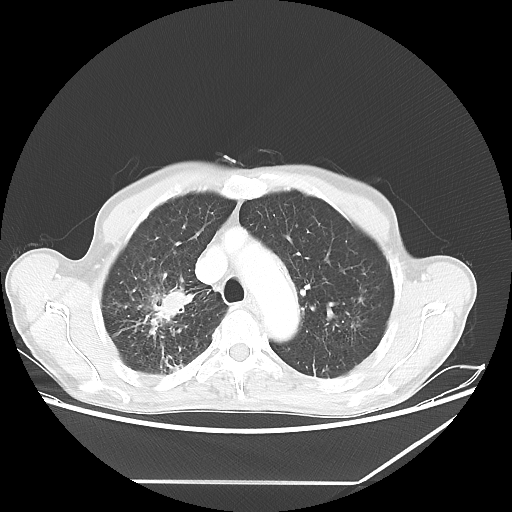
Chest CT, one axial slice. Position 48 of 65 along the scan axis. Reconstruction kernel LUNG. 80 kVp. Lung window (W 1500 / L -600 HU). 5 mm slice thickness. 512 × 512 image matrix, field of view 397 × 397 mm. Male patient, age 68 years. Case-level facts recorded for this patient, not image findings: clinical TNM (as recorded): T3 N3 M0.
Outlined on this slice (rectangle marked by the reading radiologist):
- lung tumour (recorded histology: adenocarcinoma): bounding box (x1, y1, x2, y2) in pixels: (136, 278, 195, 333)